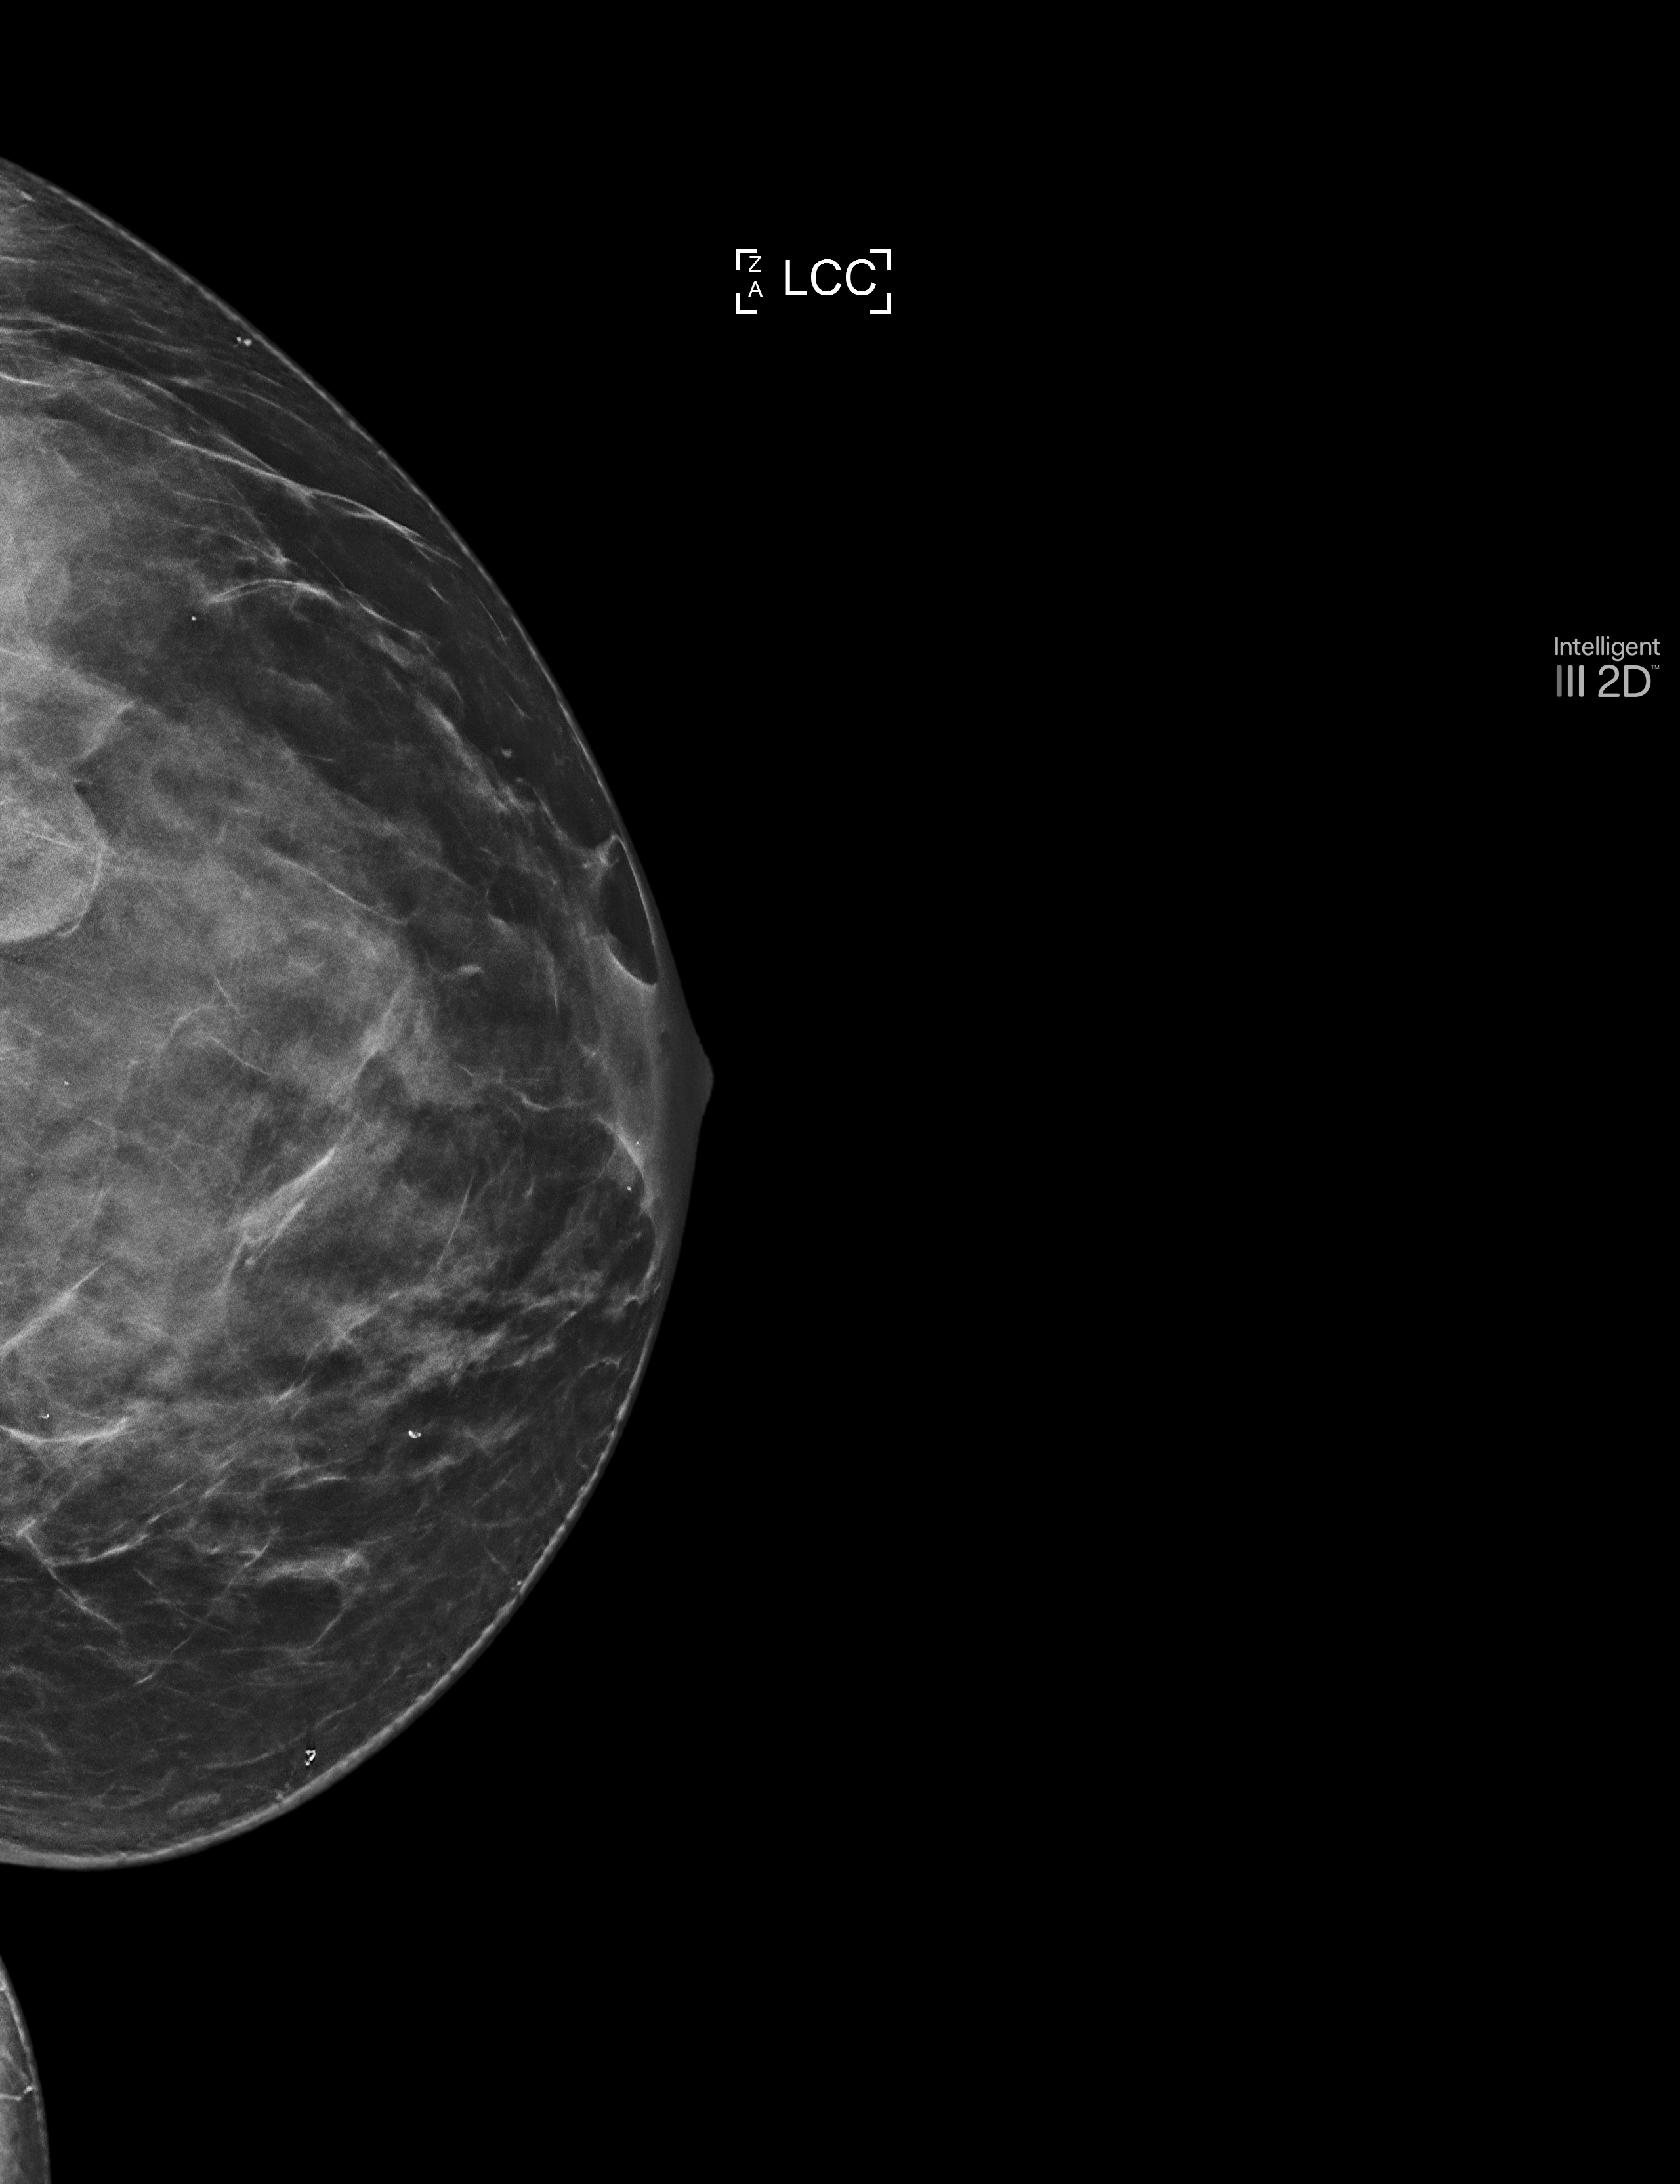
Annual screening mammography examination.
Image type: synthesized 2-D view from tomosynthesis. Breast: left. Projection: CC view.